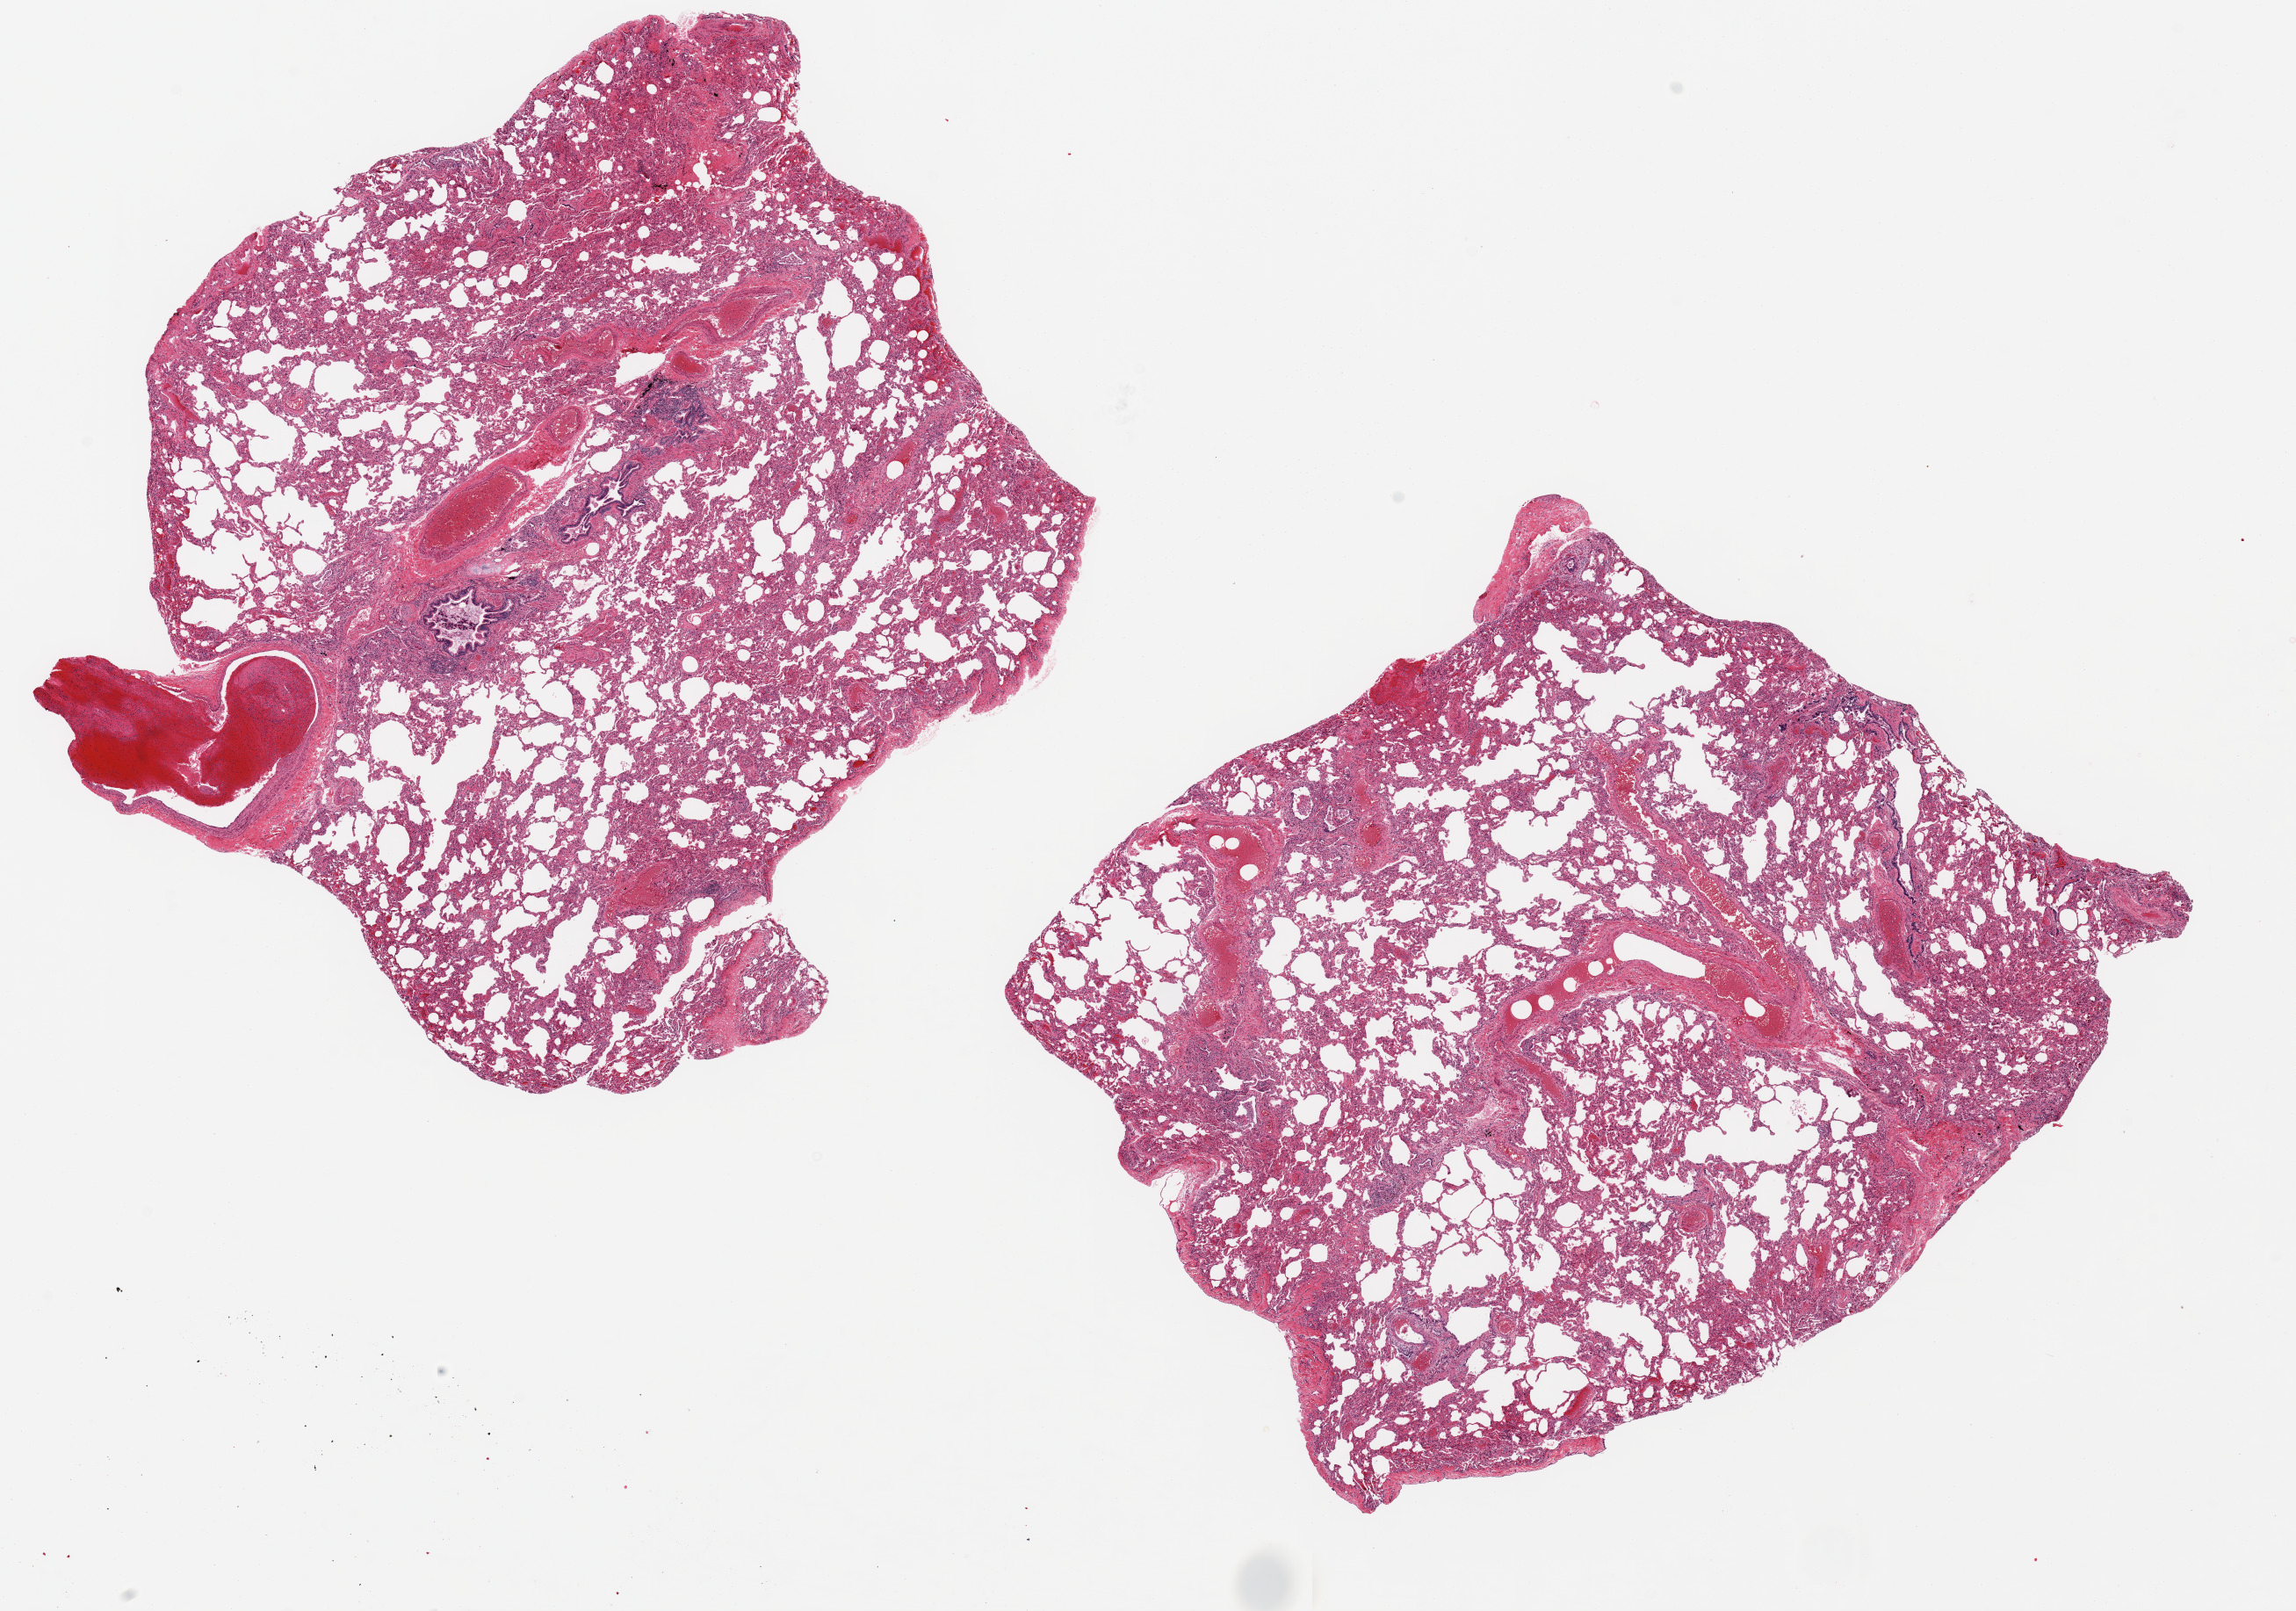
Digitized hematoxylin and eosin (H&E)-stained section — shown as a low-resolution overview of the whole scanned area (about 20.7 x 14.5 mm); PAXgene-fixed, paraffin-embedded tissue; section of lung (target tissue); donor tissue sample.
Reviewer comment on this tissue sample: 2 ~8x6.5mm aliquots, areas of interstitial fibrosis/inflammation.